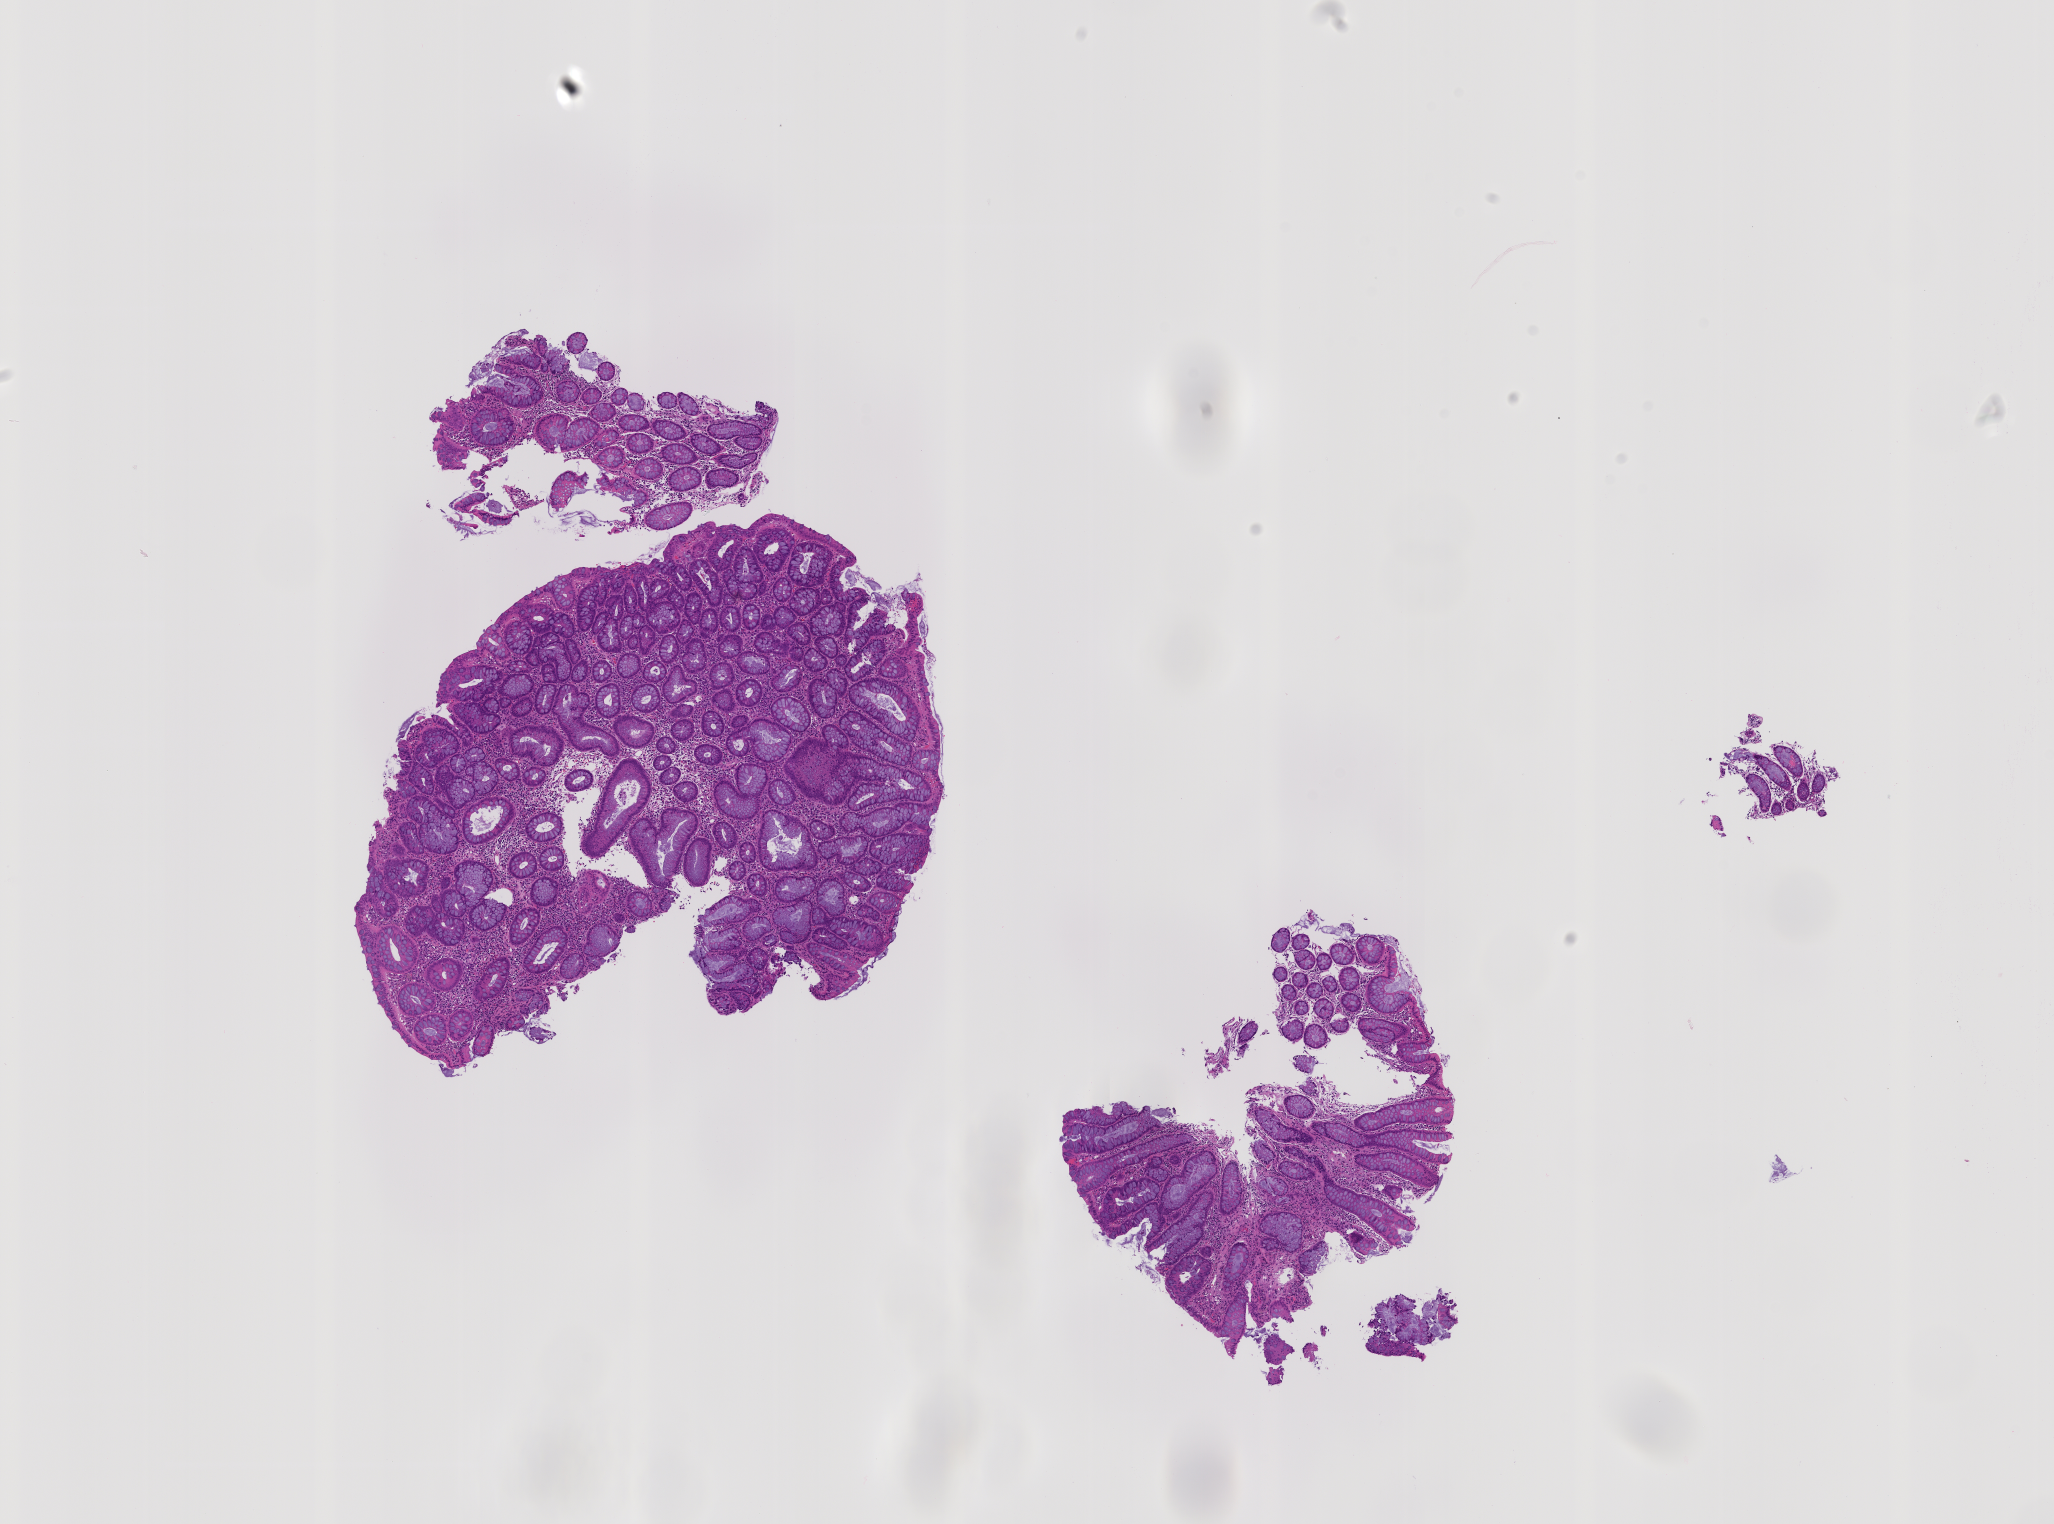
Whole-slide image, haematoxylin and eosin stain: colon biopsy, whole scanned area (about 8.2 x 6.1 mm) shown as a low-resolution overview; formalin-fixed, paraffin-embedded (FFPE) tissue; site: transverse colon. Male patient.
Lesion category (as recorded): premalignant.